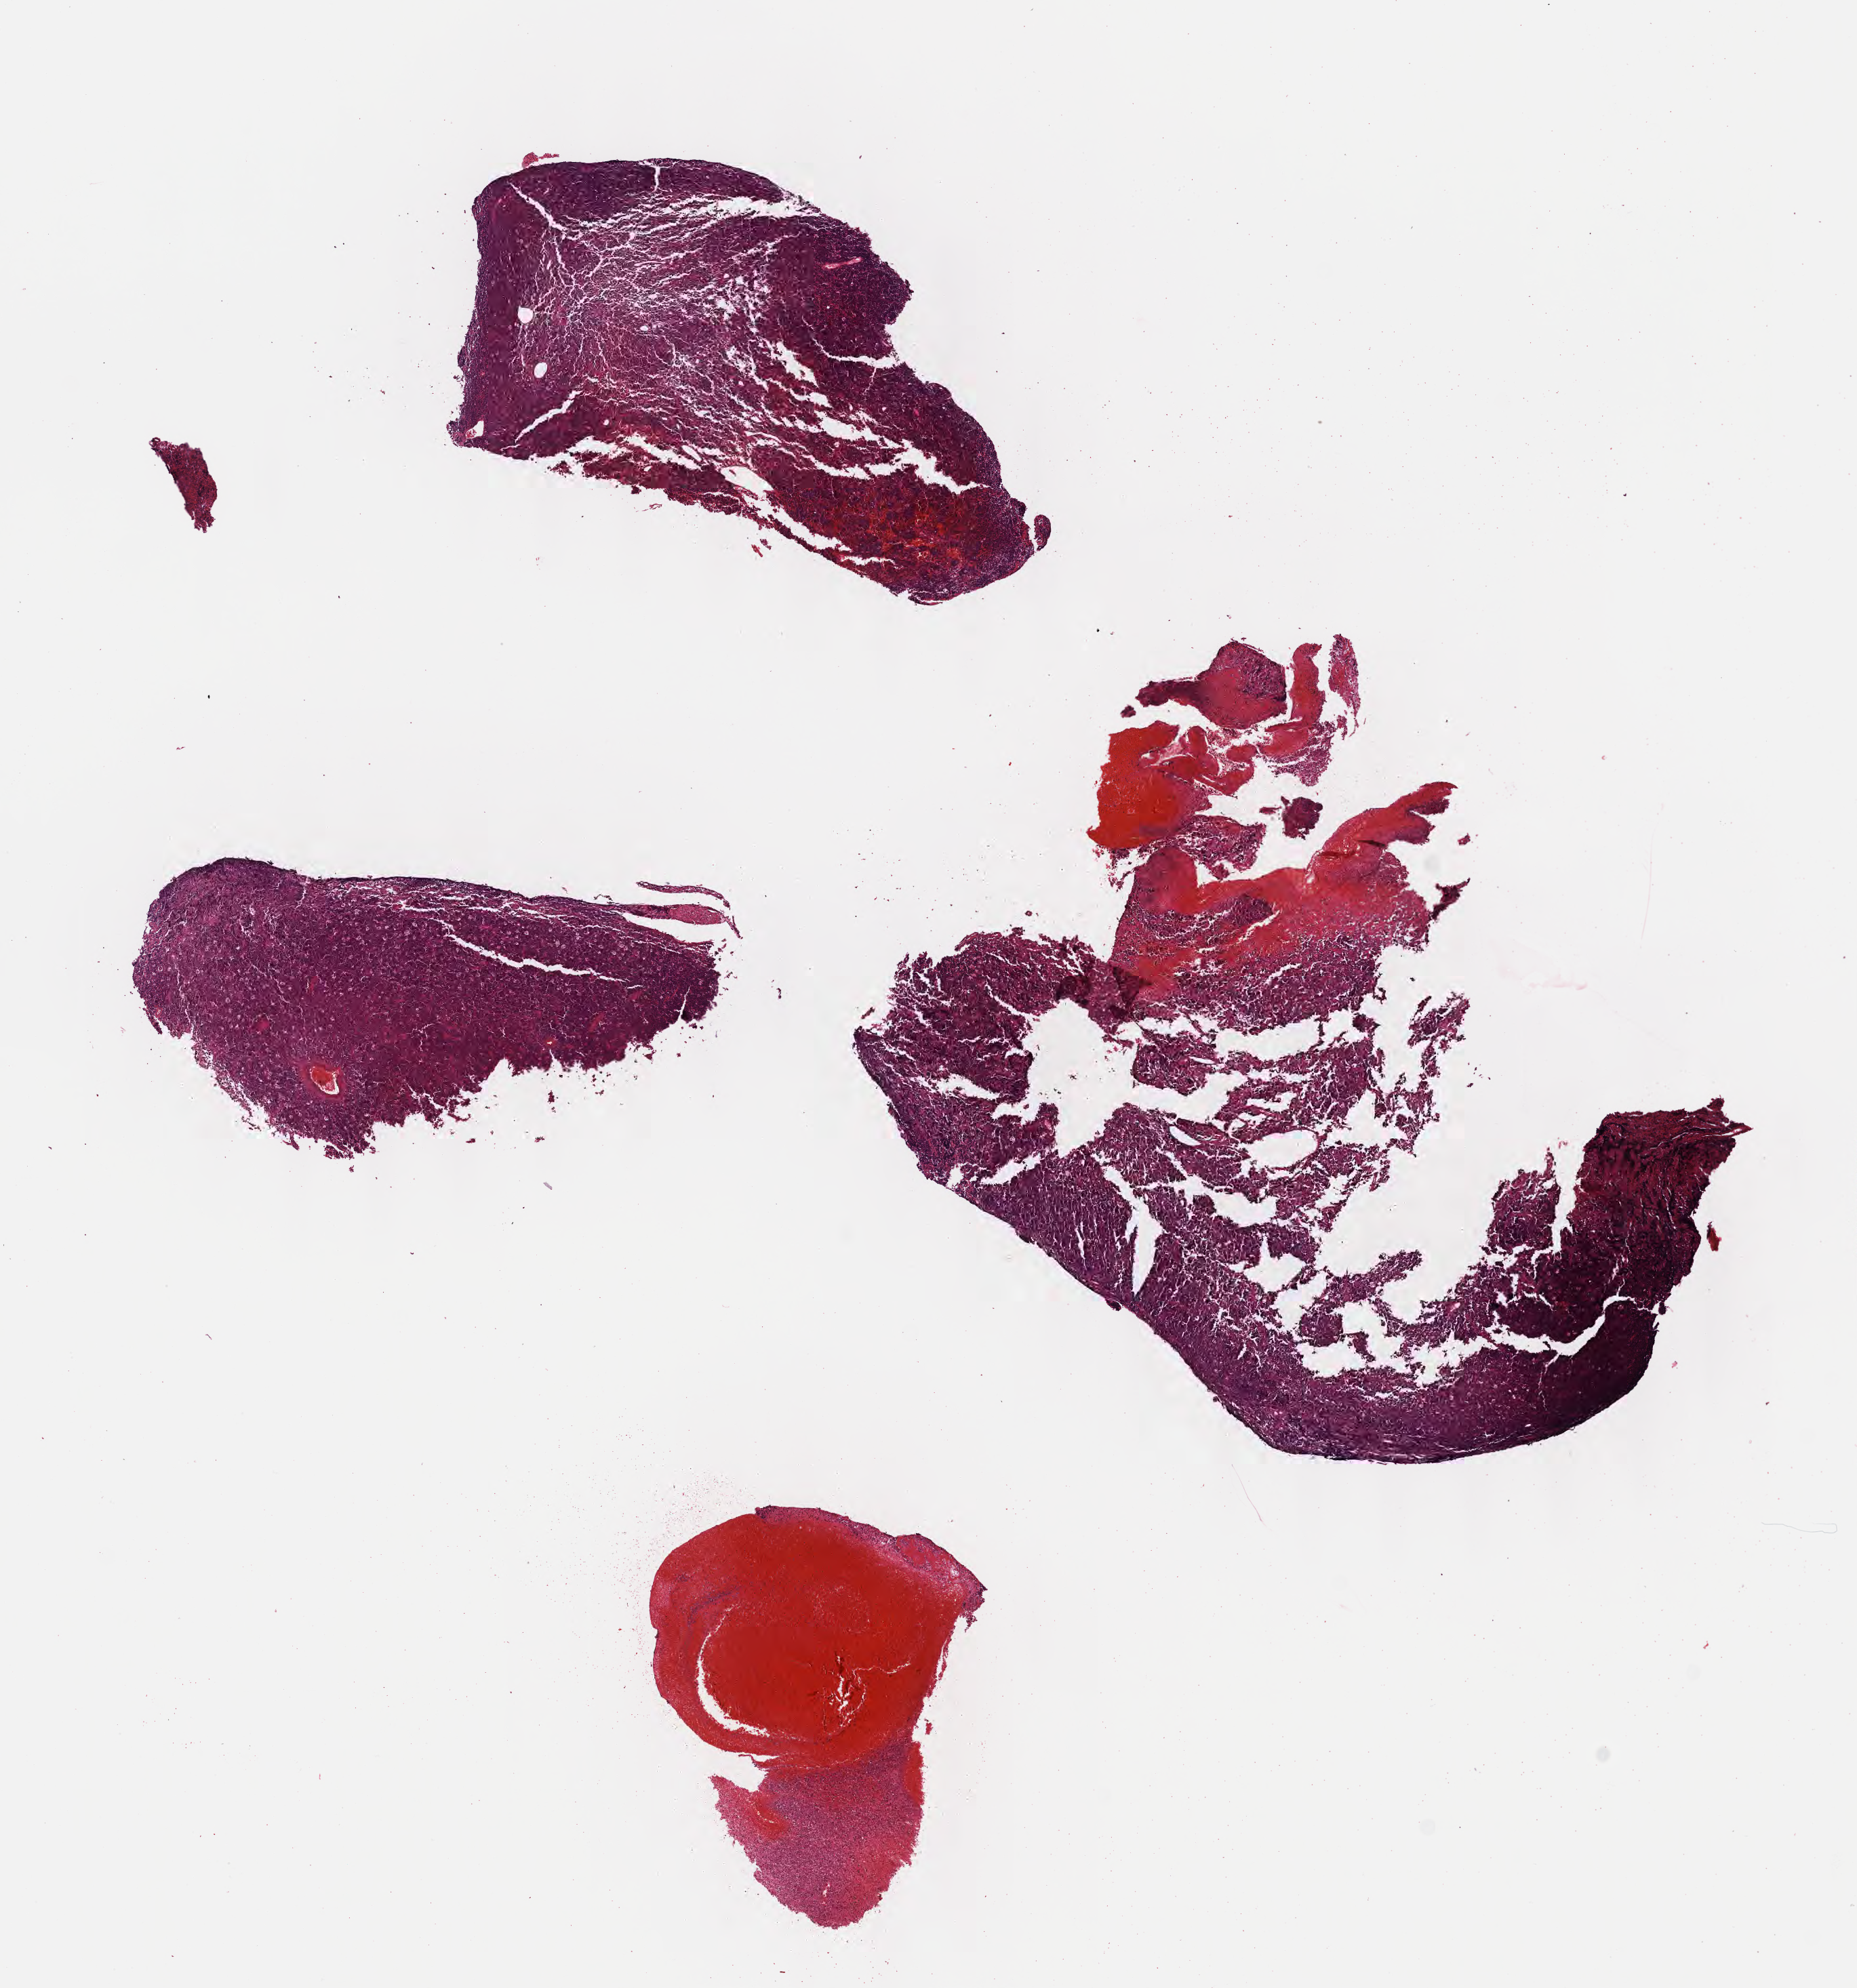
Digitized H&E-stained section — a low-resolution overview of the entire scanned area, about 11.1 x 11.8 mm, formalin-fixed paraffin-embedded section, primary tumor. Patient: male, age 10 years. Pathologist review of this section (percent, as recorded): tumor cells 90%, tumor nuclei 95%, stromal cells 5%, necrosis 5%, normal cells 0%. Inflammatory infiltration, as recorded: lymphocyte infiltration 70%, monocyte infiltration 15%, neutrophil infiltration 5%.
Diagnosis: Burkitt lymphoma, NOS. Section: top of the tissue portion. Ann Arbor stage (patient): Stage IV.